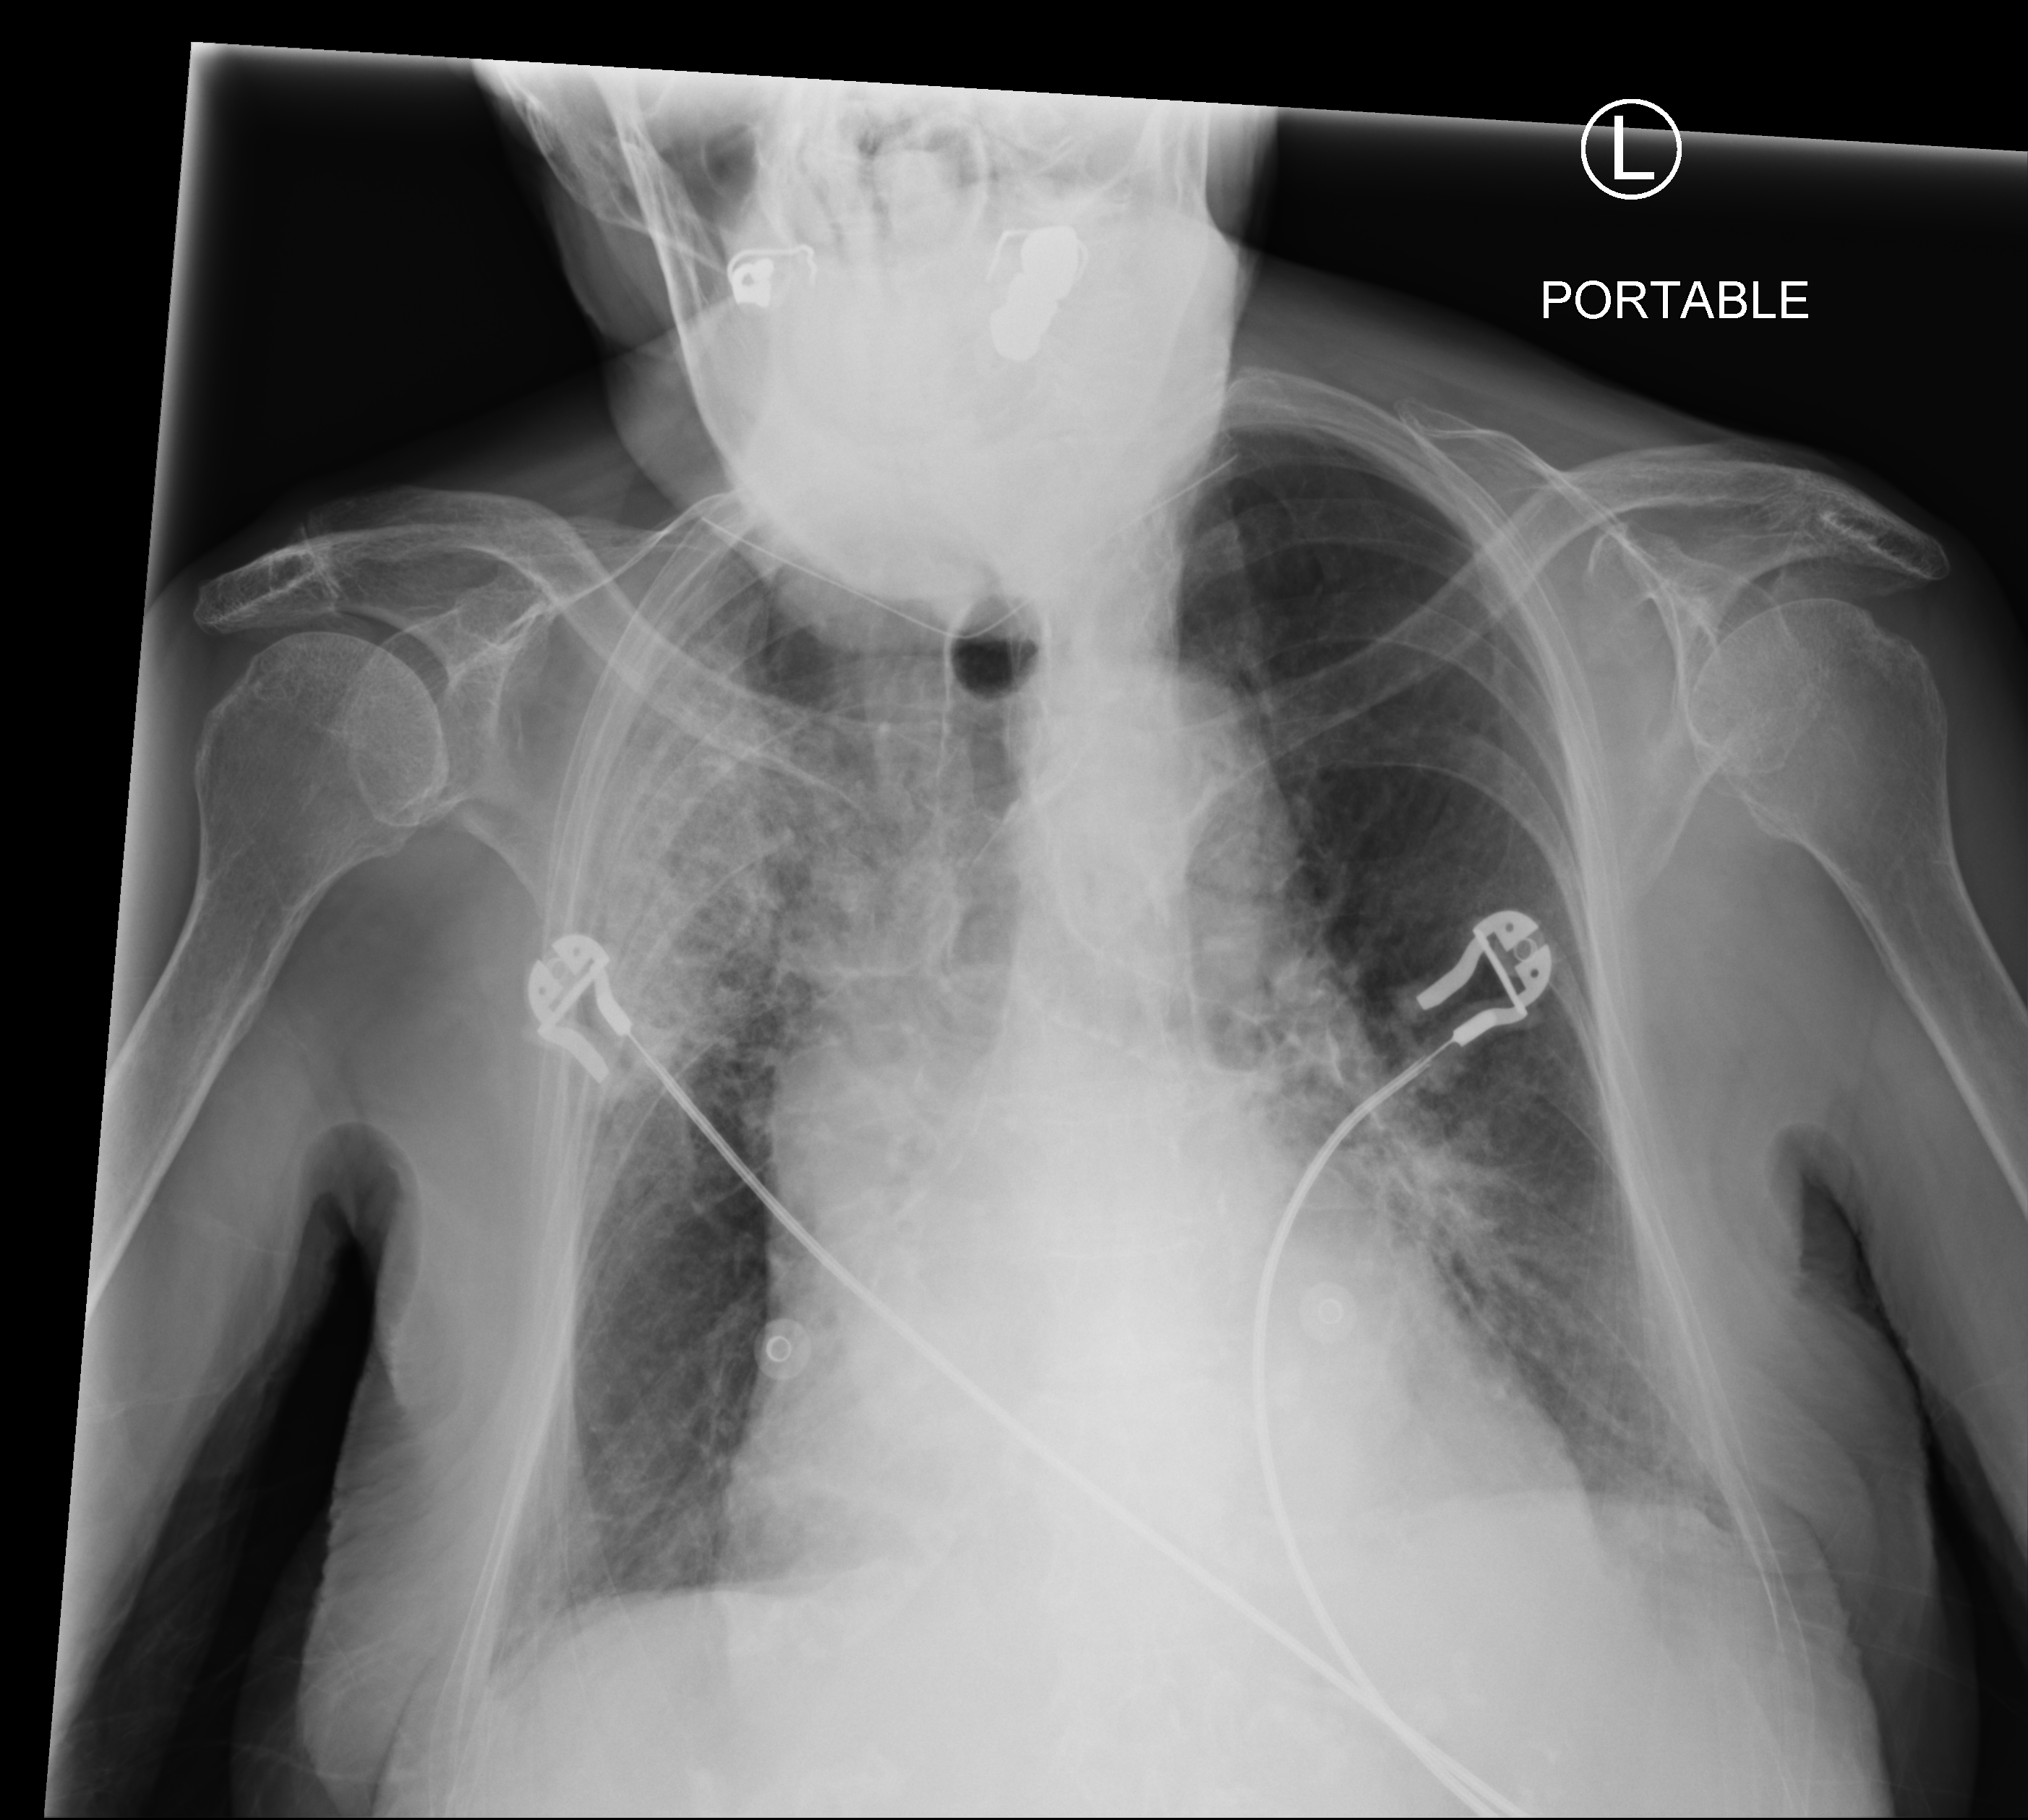
Portable chest radiograph, anteroposterior (AP) projection. Patient hospitalised with COVID-19; female, aged 75–90 years.
Hospital-stay facts (about this admission, not read from this image; timing relative to this image not recorded):
- mechanically ventilated during this hospital stay: no
- admitted to intensive care during this hospital stay: no